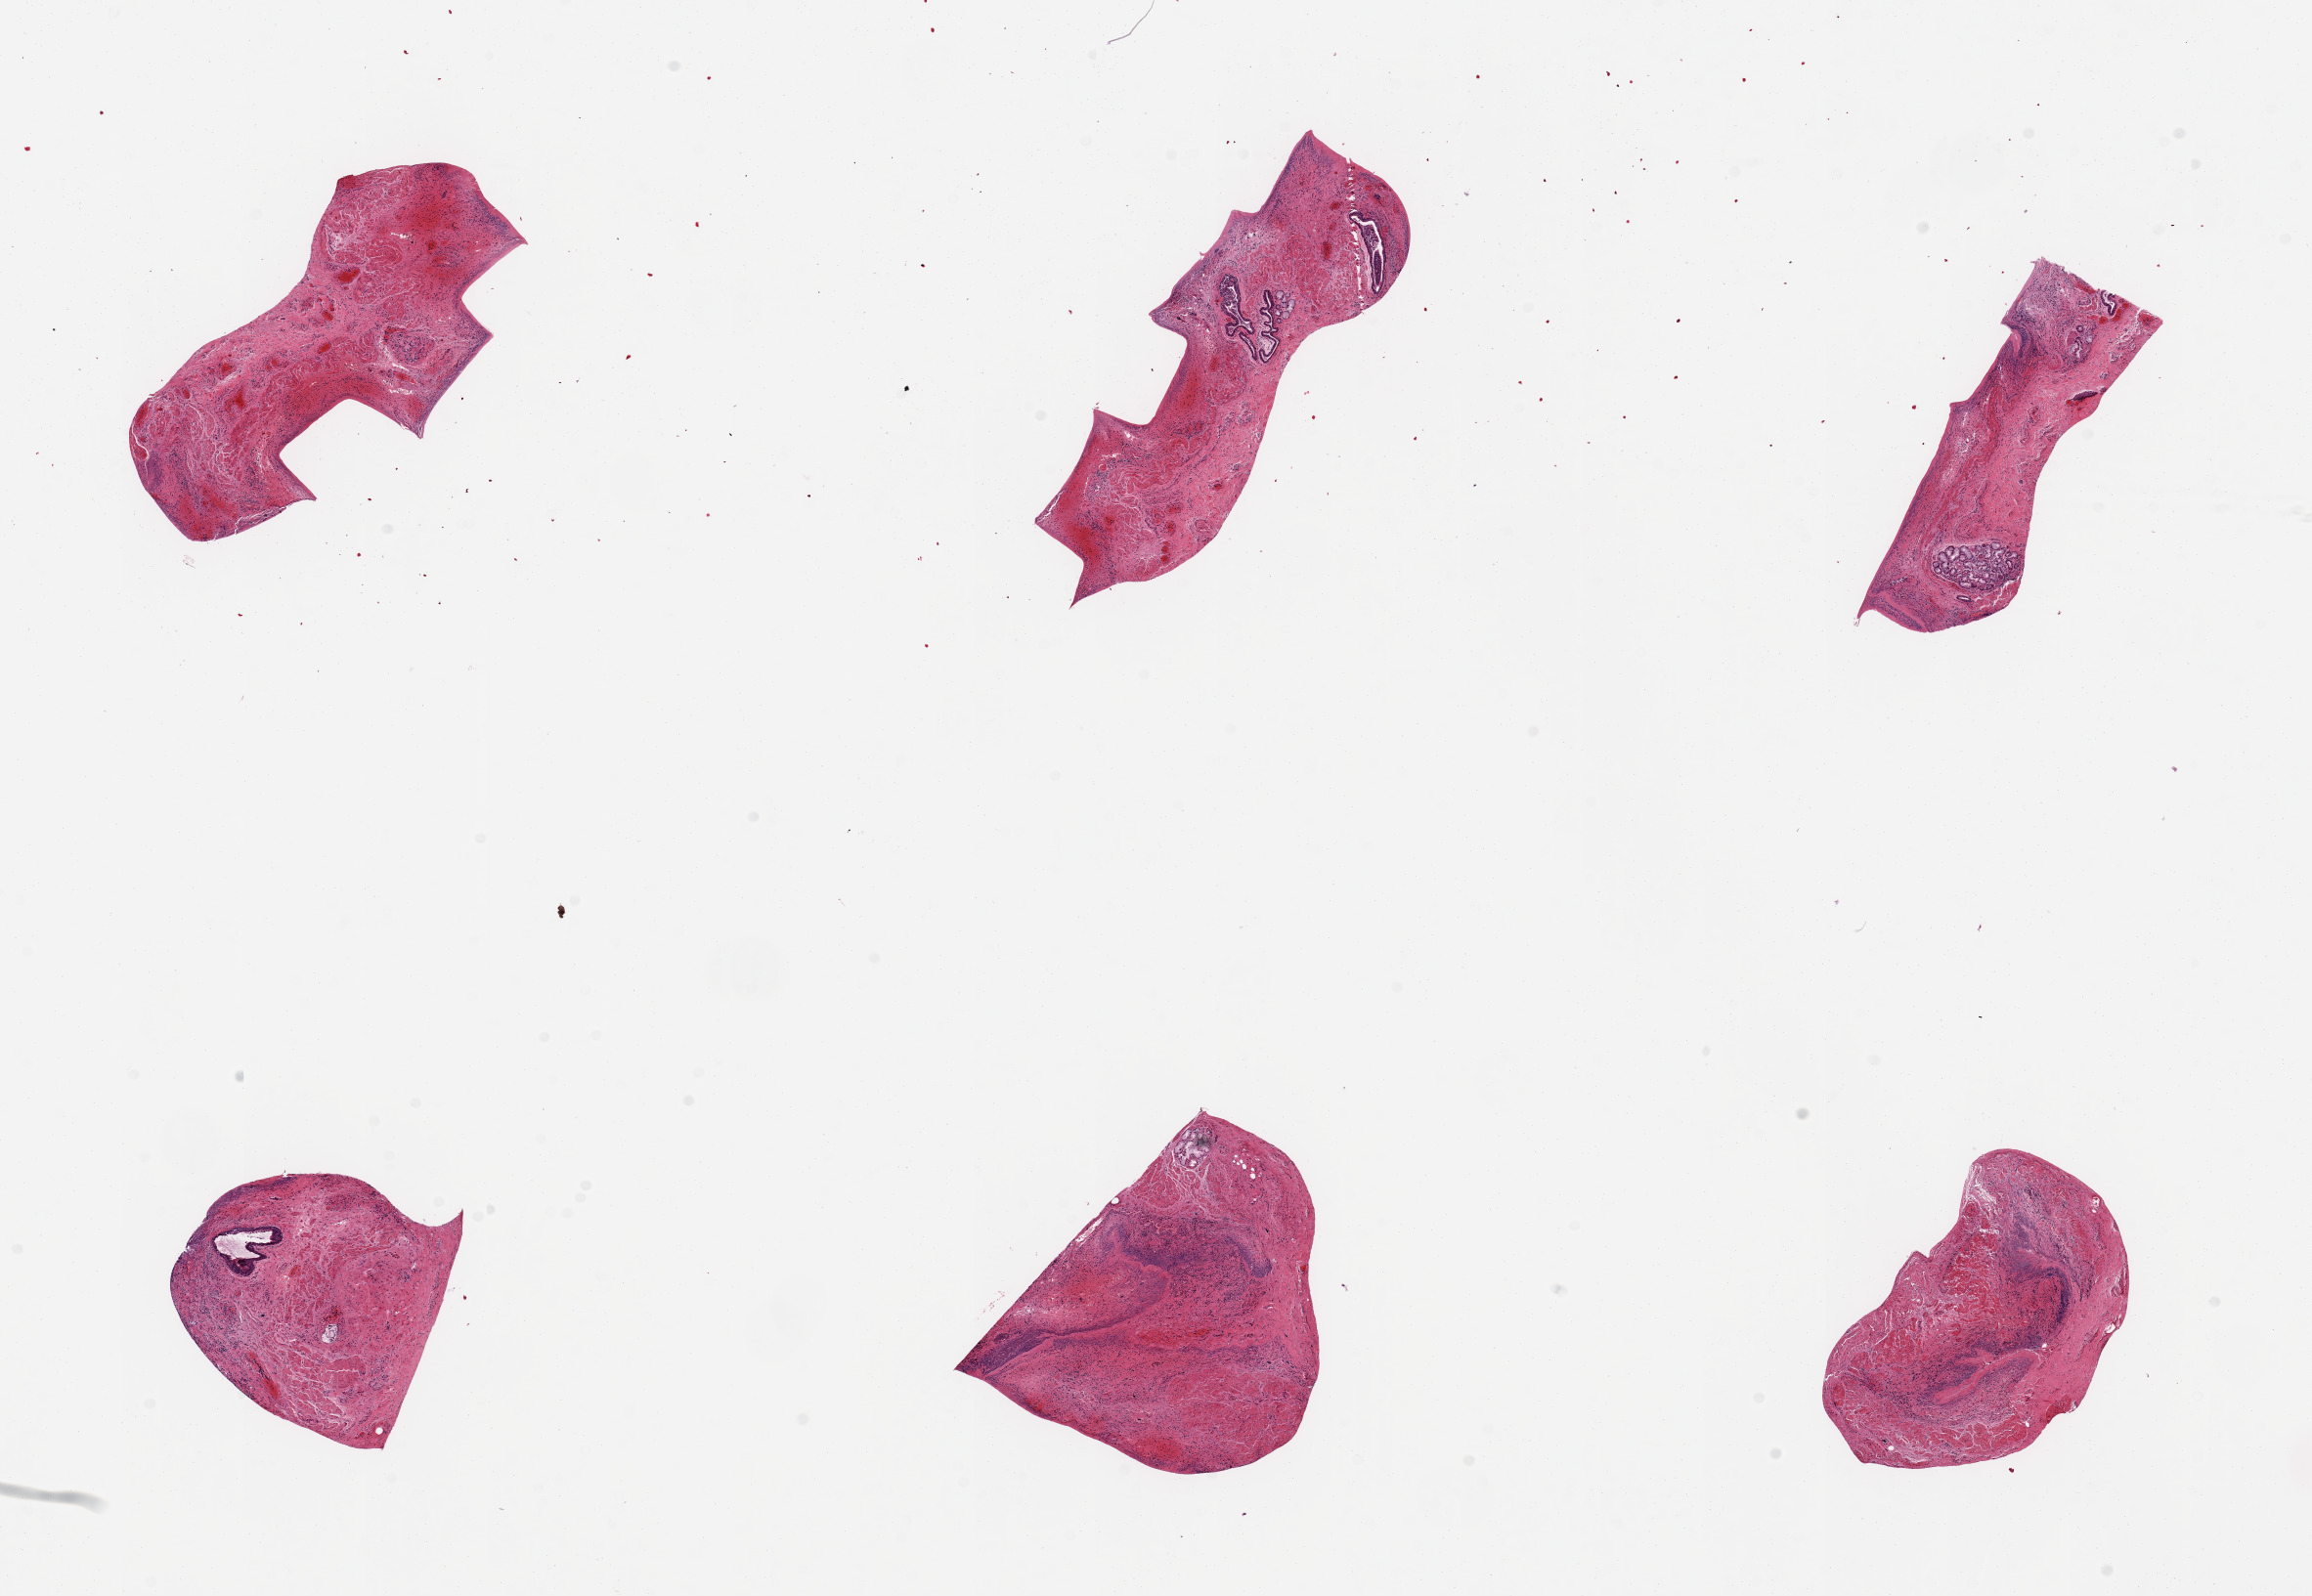
Haematoxylin and eosin whole-slide image, shown as a low-resolution overview of the whole scanned area (about 18.7 x 12.9 mm); PAXgene-fixed paraffin-embedded (PFPE) section; section of esophageal mucous membrane (target tissue); tissue donor sample. Female donor.
• review note (as recorded): 6 pieces, squamous mucosa largely sloughed; residual submucosal mucus glands; a few sqauamous mucosal herniations noted